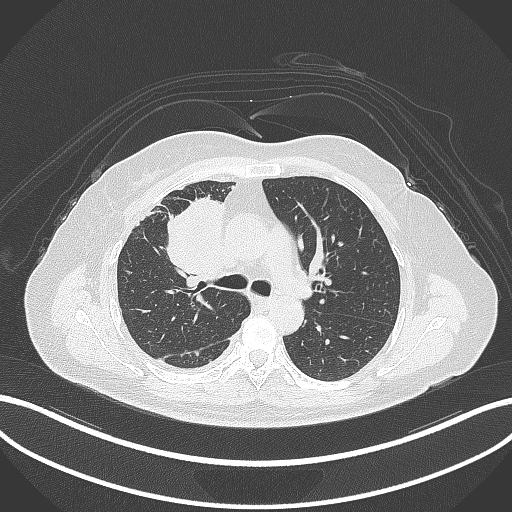
Chest CT, one axial slice. Slice 181 of 305 in the series (ordered by position). Reconstruction kernel B70f. 120 kVp. Lung window (W 1500 / L -600 HU). 512 × 512 image matrix. Patient: female, 52 years. From the clinical record (not read from this slice): clinical TNM (as recorded): T3 N1 M1.
Structures marked on this image (bounding box drawn by a radiologist):
- lung tumour (recorded histology: adenocarcinoma): bounding box <161,194,233,280> (left, top, right, bottom; pixels)